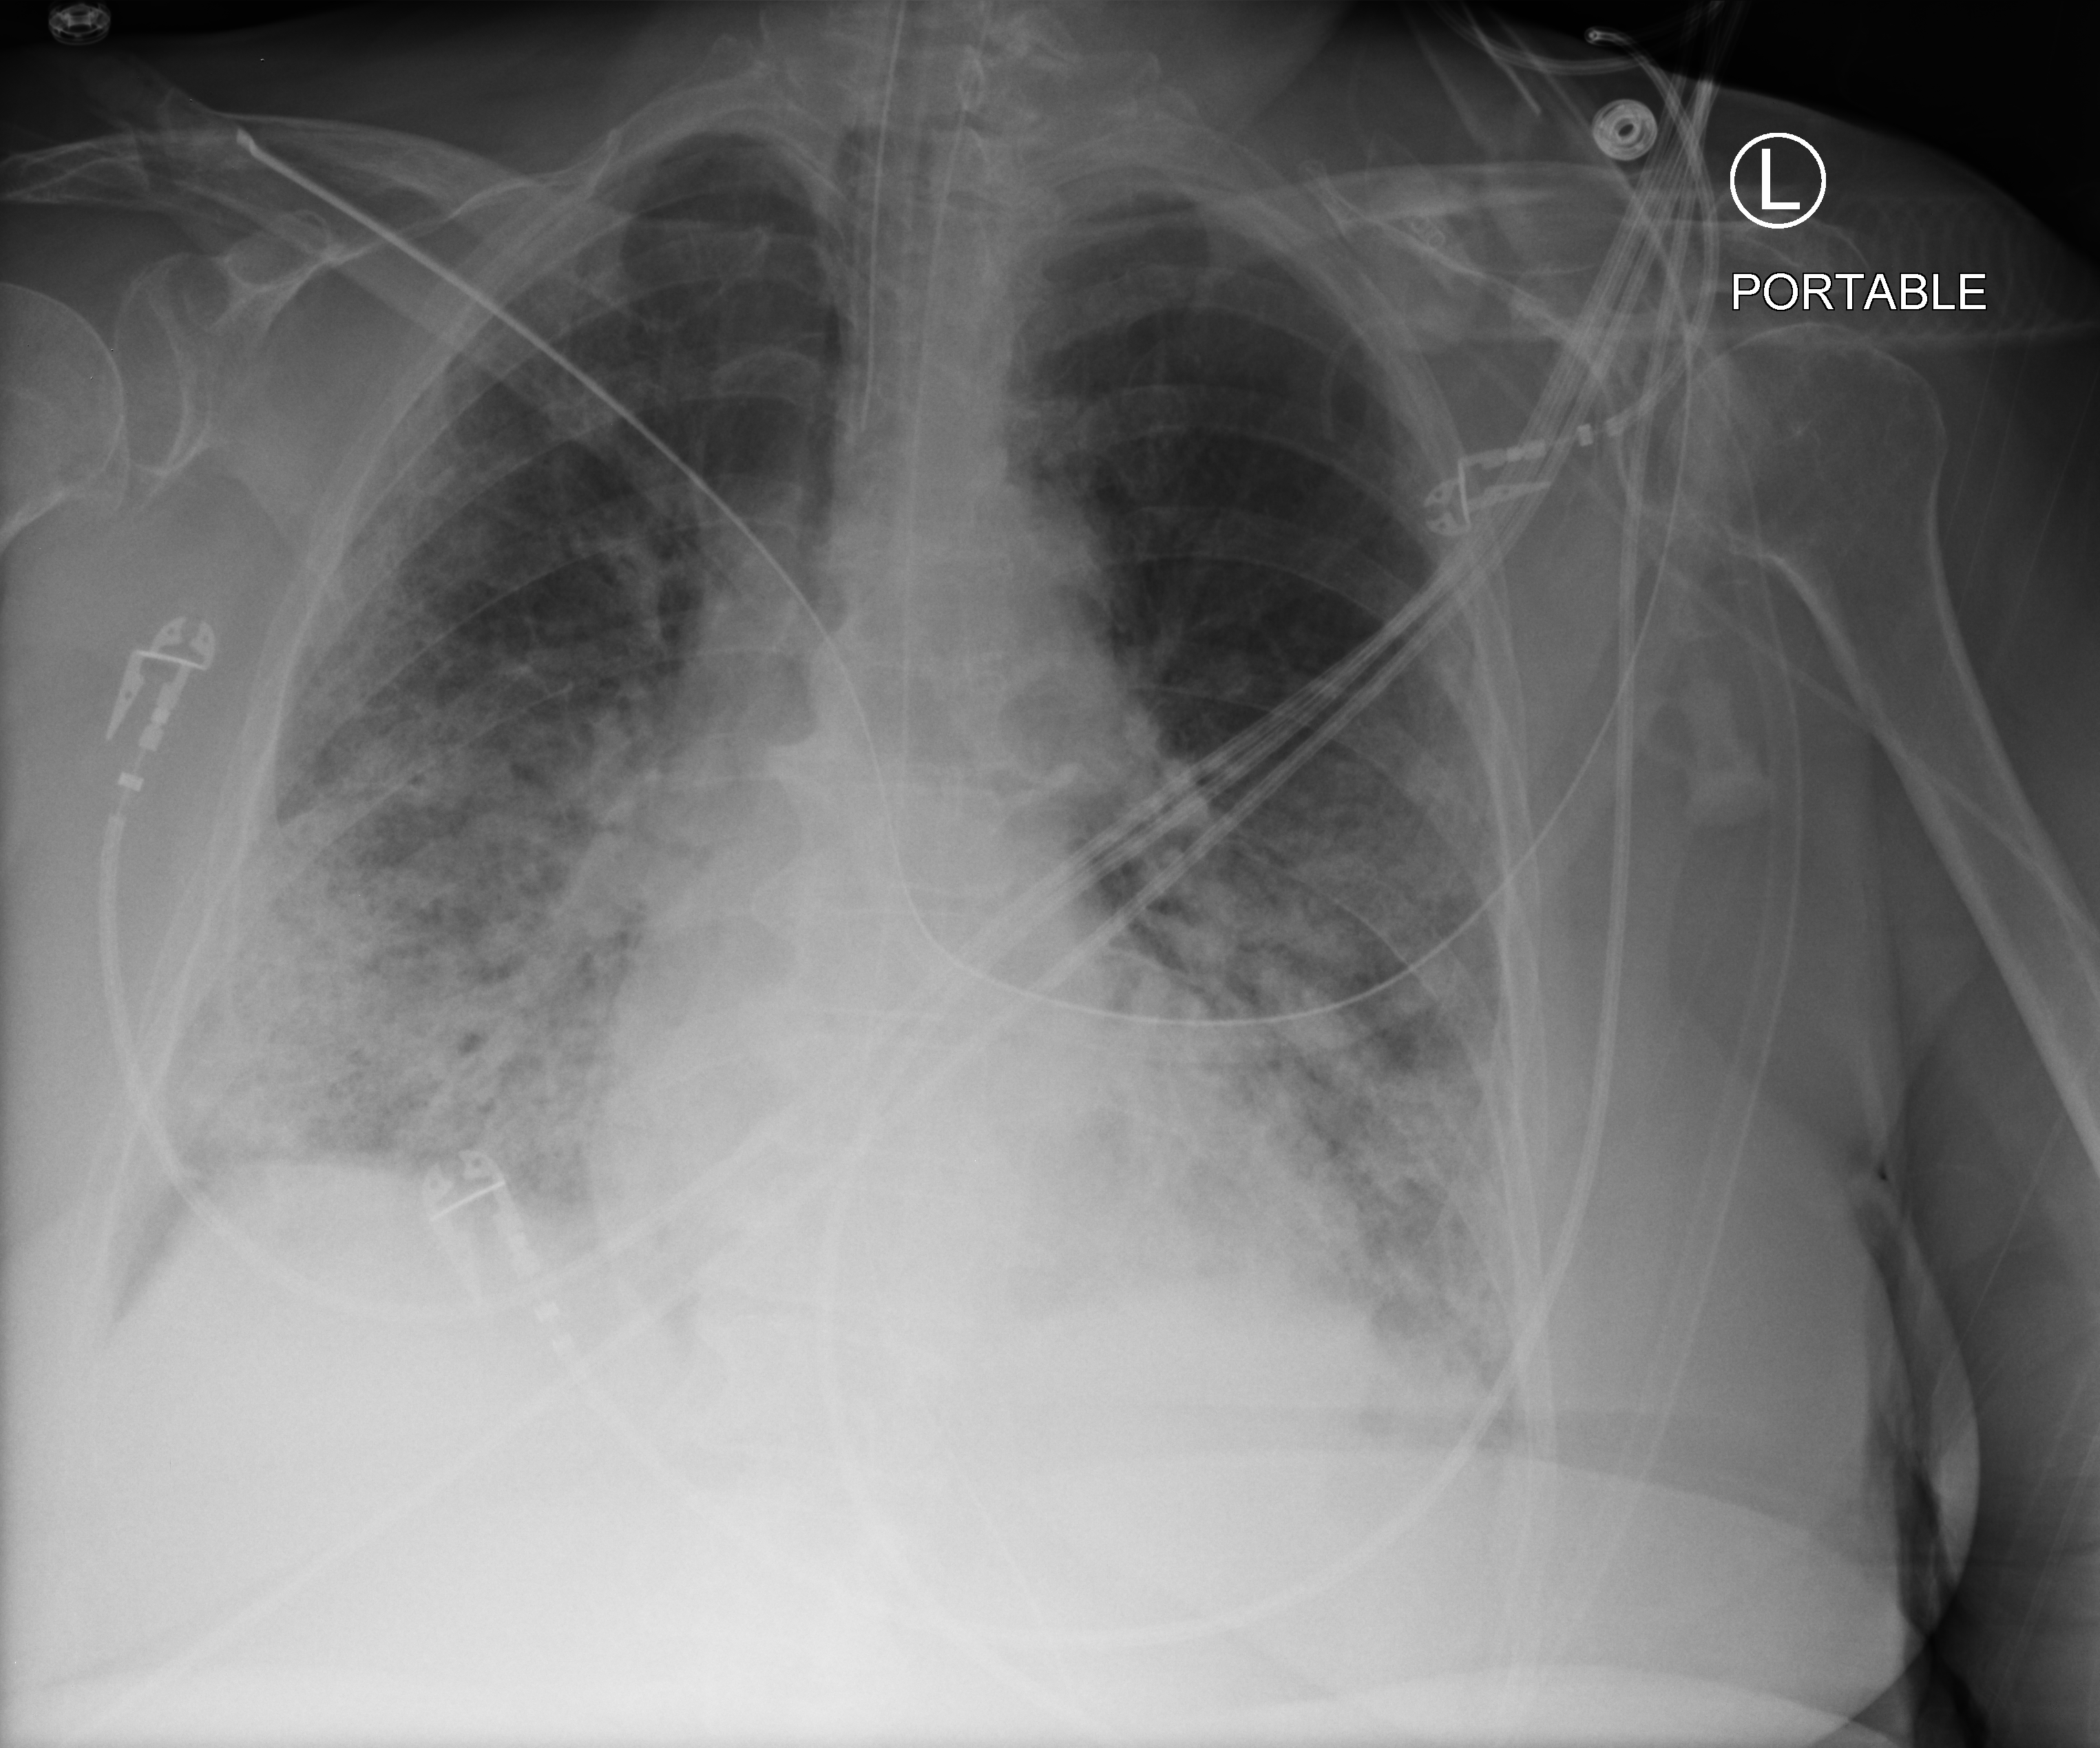
Portable chest radiograph; anteroposterior (AP) projection. Female patient hospitalised with COVID-19, age 75–90 years.
From the hospital-stay record, not from the radiograph (when in the stay this image was taken is not recorded):
- diabetes (admission record): no
- admitted to intensive care during this hospital stay: no
- mechanically ventilated during this hospital stay: yes